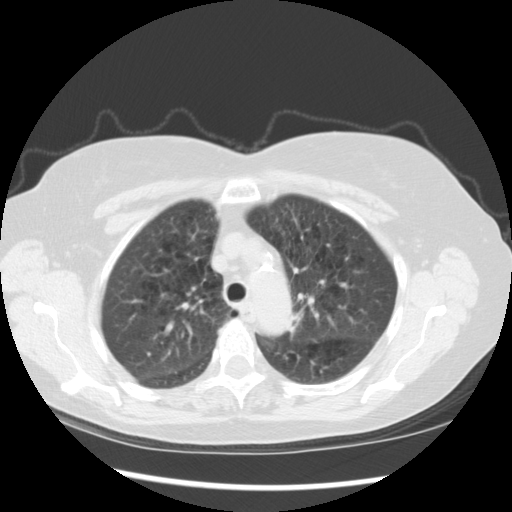
Low-dose screening chest CT, axial slice; baseline screening round; lung window (W 1500 / L -600 HU); 2.5 mm slice thickness; 120 kVp; slice 97 of 123 in the series. Female, age 70 years at enrolment. Current smoker at enrolment.
- Lesion marked by an expert reader, bounding box (x1, y1, x2, y2) in pixels: (274, 300, 320, 351).
- No non-calcified nodule or mass ≥4 mm was recorded by the screening reader at this exam.
- Official screen result: negative screen, minor abnormalities not suspicious for lung cancer.
- Lung cancer was diagnosed 757 days after this screen (after the third annual screen): neoplasm, malignant, left upper lobe, stage IIIB (AJCC 6th edition), 40 mm at pathology.